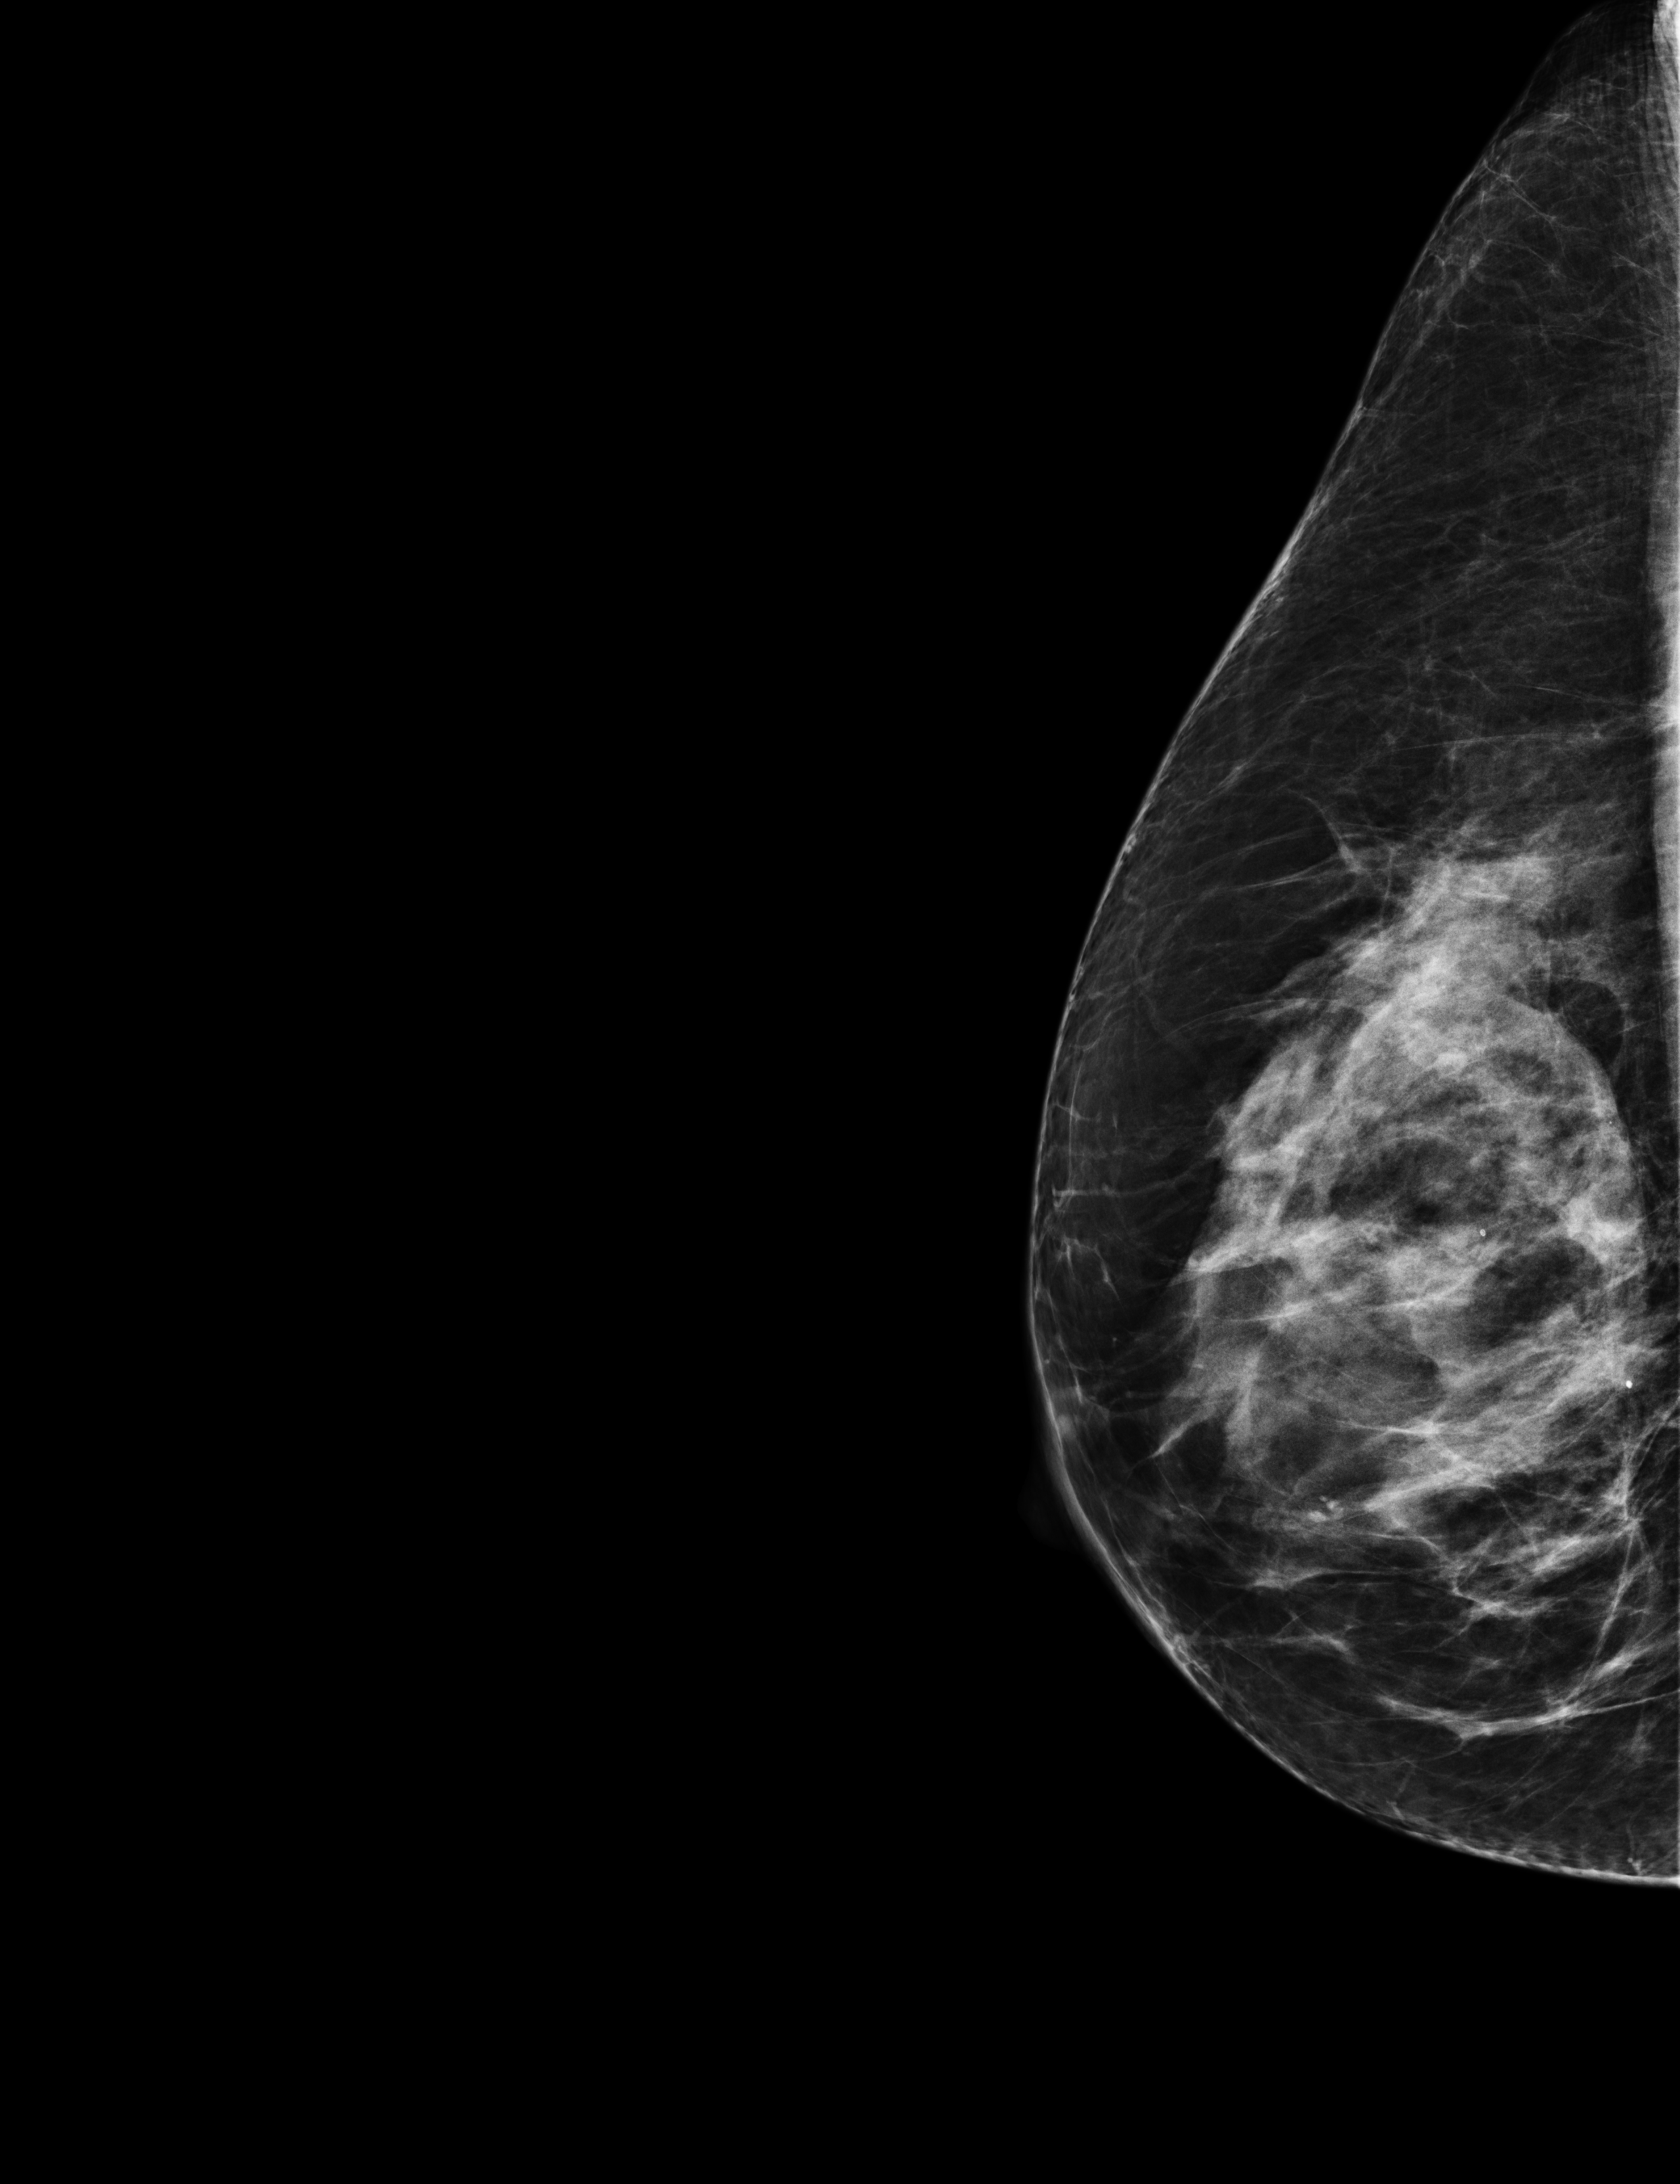
Full-field digital mammogram (FFDM), right breast, exaggerated CC view (lateral), annual screening mammography examination, system: Selenia Dimensions. Patient aged 59 years (female).
Breast density at the screening exam (both breasts): heterogeneously dense (BI-RADS density category c). Final BI-RADS category for the screening round (tomosynthesis exam, both breasts): category 2. Recall: no recall after this screen.